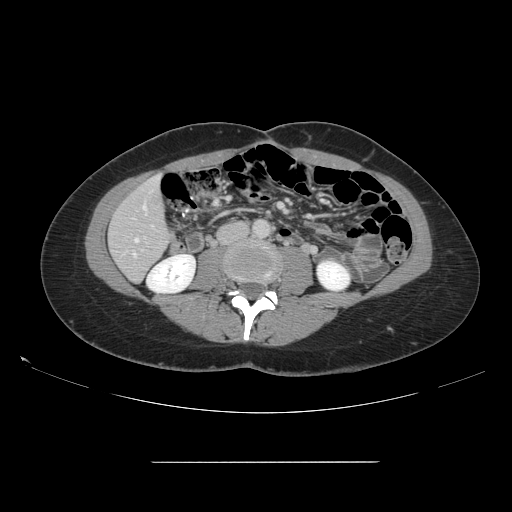
Contrast-enhanced abdominal CT, one axial slice; position 37 of 151 along the scan axis; 120 kVp; soft-tissue window (W 400 / L 40 HU); 512 × 512 image matrix. Female patient, age 46 years. Case-level facts recorded for this patient, not image findings: diagnosis: colorectal cancer liver metastases, imaged before liver resection; multiple liver metastases: yes; largest metastasis: 3 cm; disease in both lobes: yes.
Outlined on this slice (manually delineated by an expert):
- hepatic veins: bounding box <135,206,146,242> (left, top, right, bottom; pixels)
- liver: <110,178,170,281>
- planned liver remnant (the part of the liver to remain after resection): <110,178,171,281>